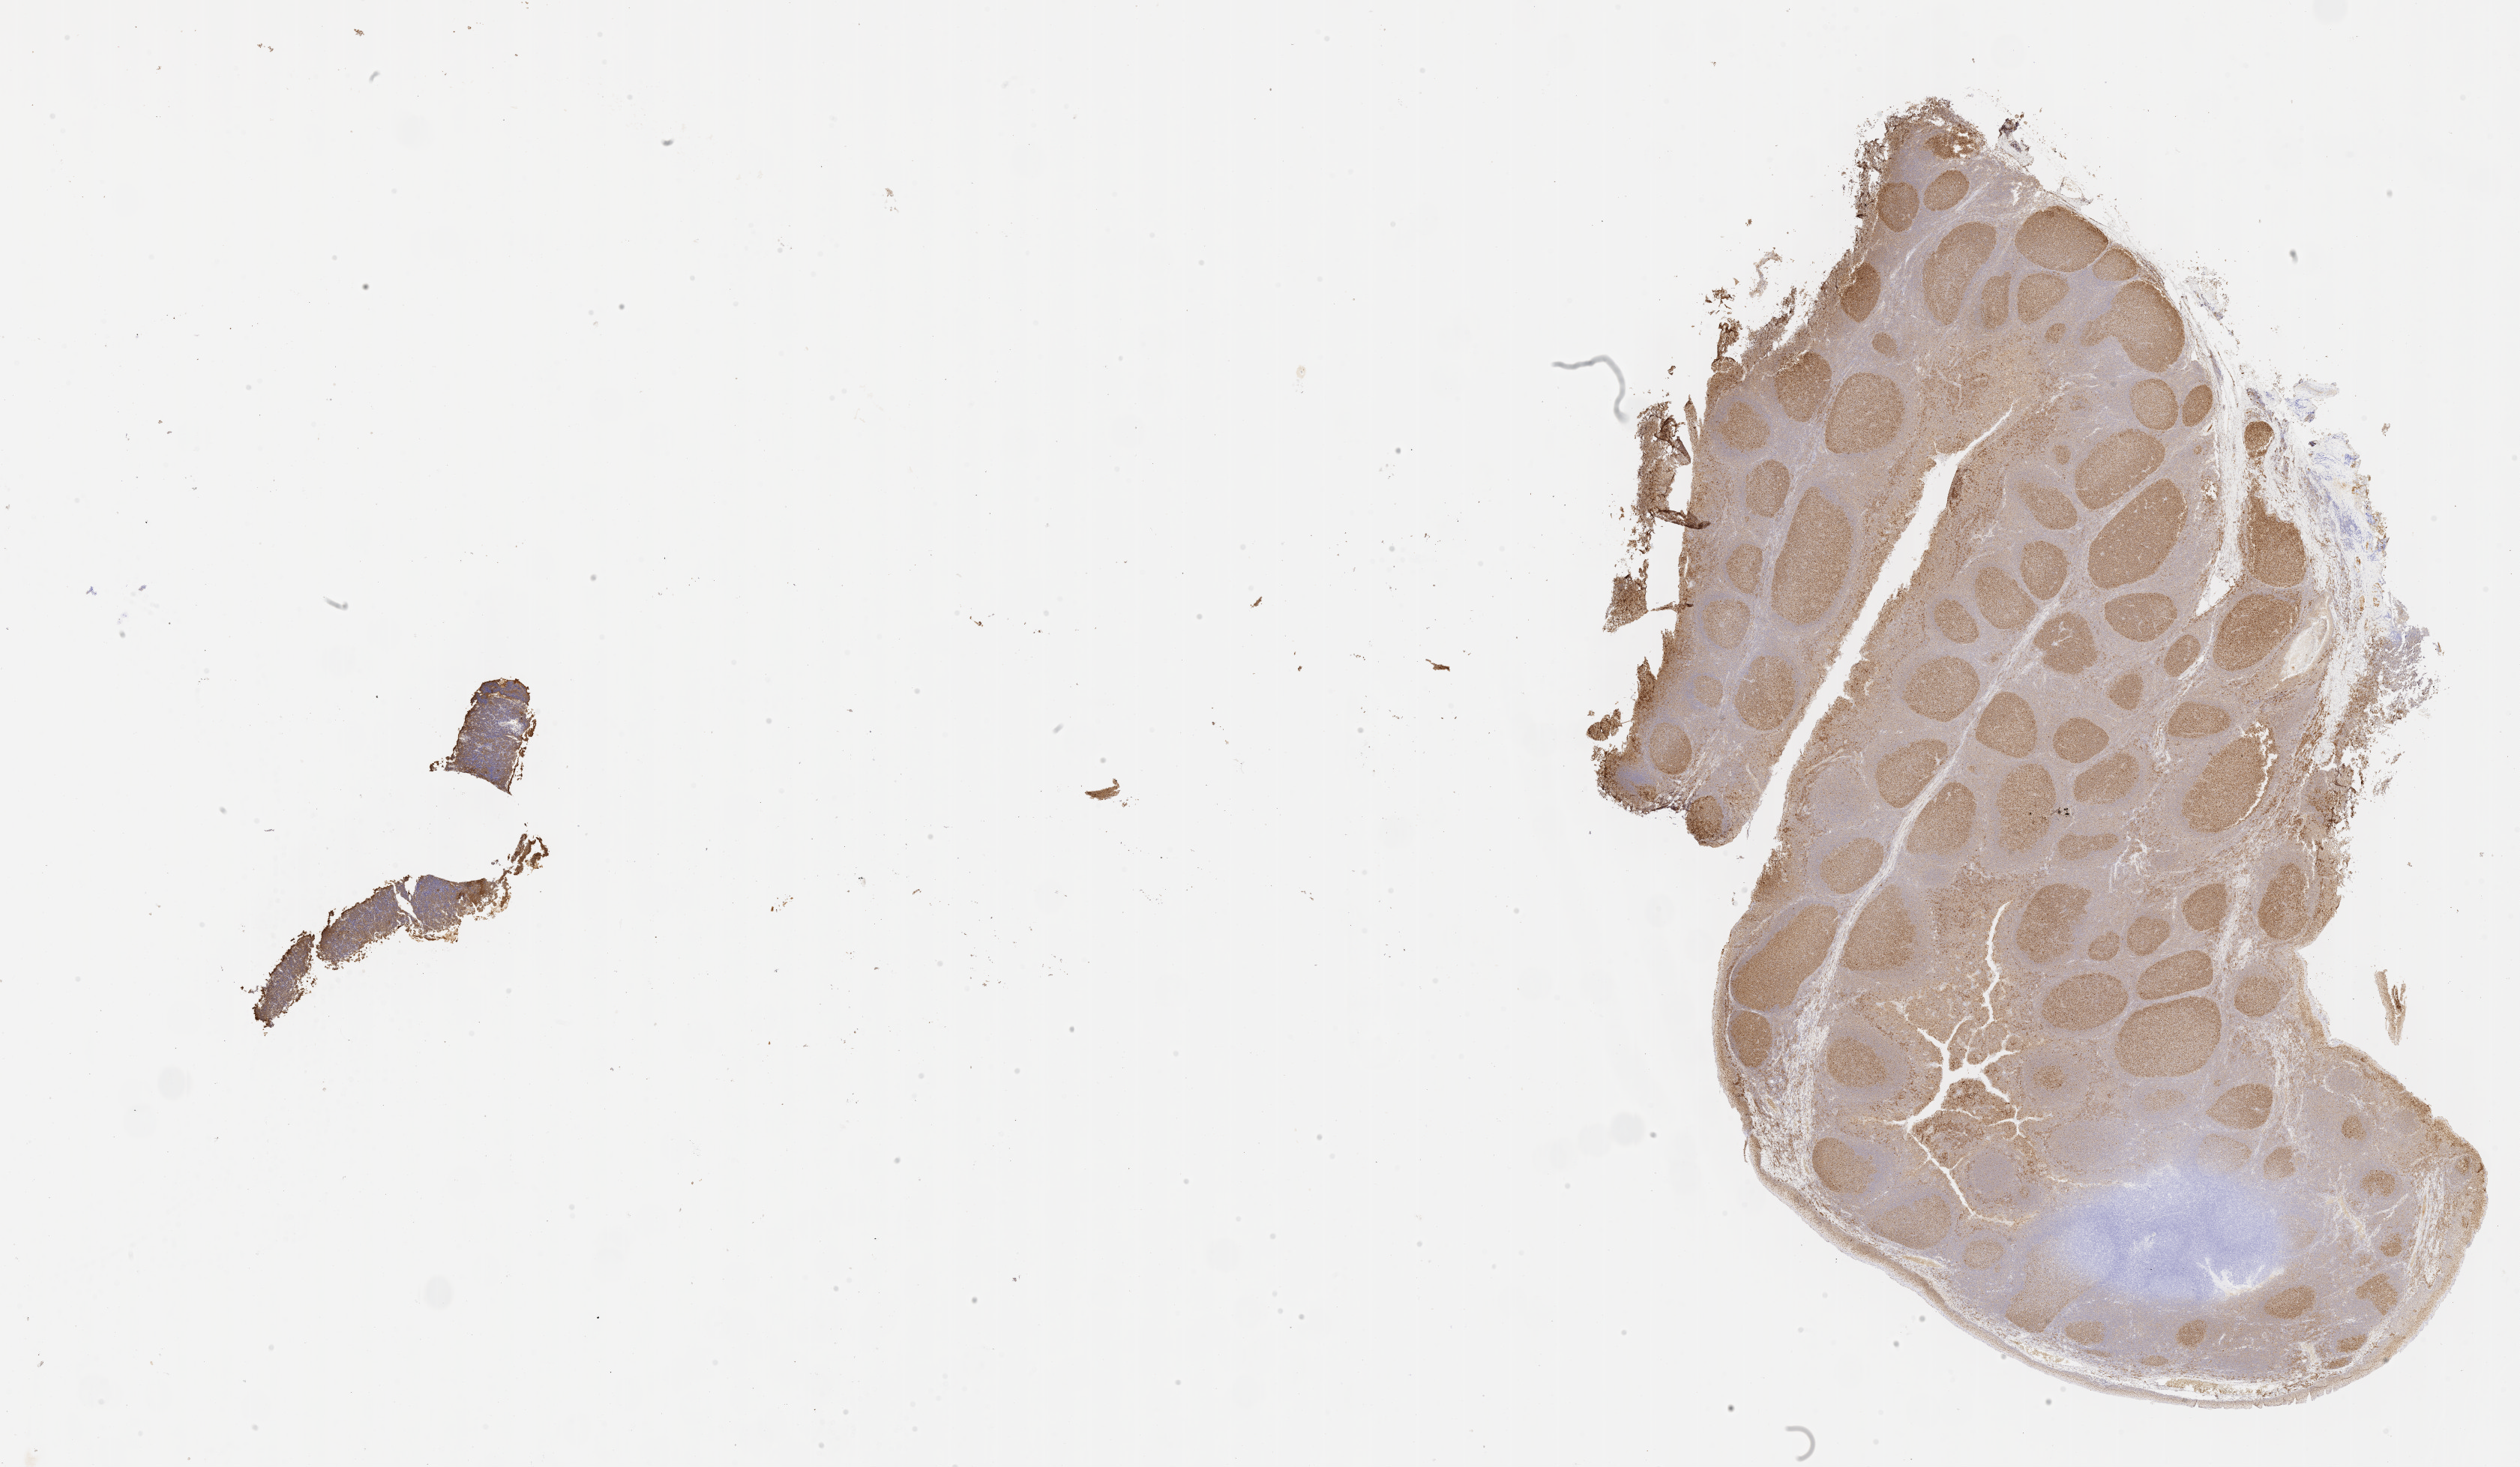
Immunohistochemistry (IHC) whole-slide image stained for BCL6 — shown as a low-resolution overview of the whole scanned area (about 27.2 x 15.8 mm); specimen: tumor tissue; site: cranium. Male patient; age at initial diagnosis 6 years.
- histologic diagnosis: Burkitt lymphoma, NOS